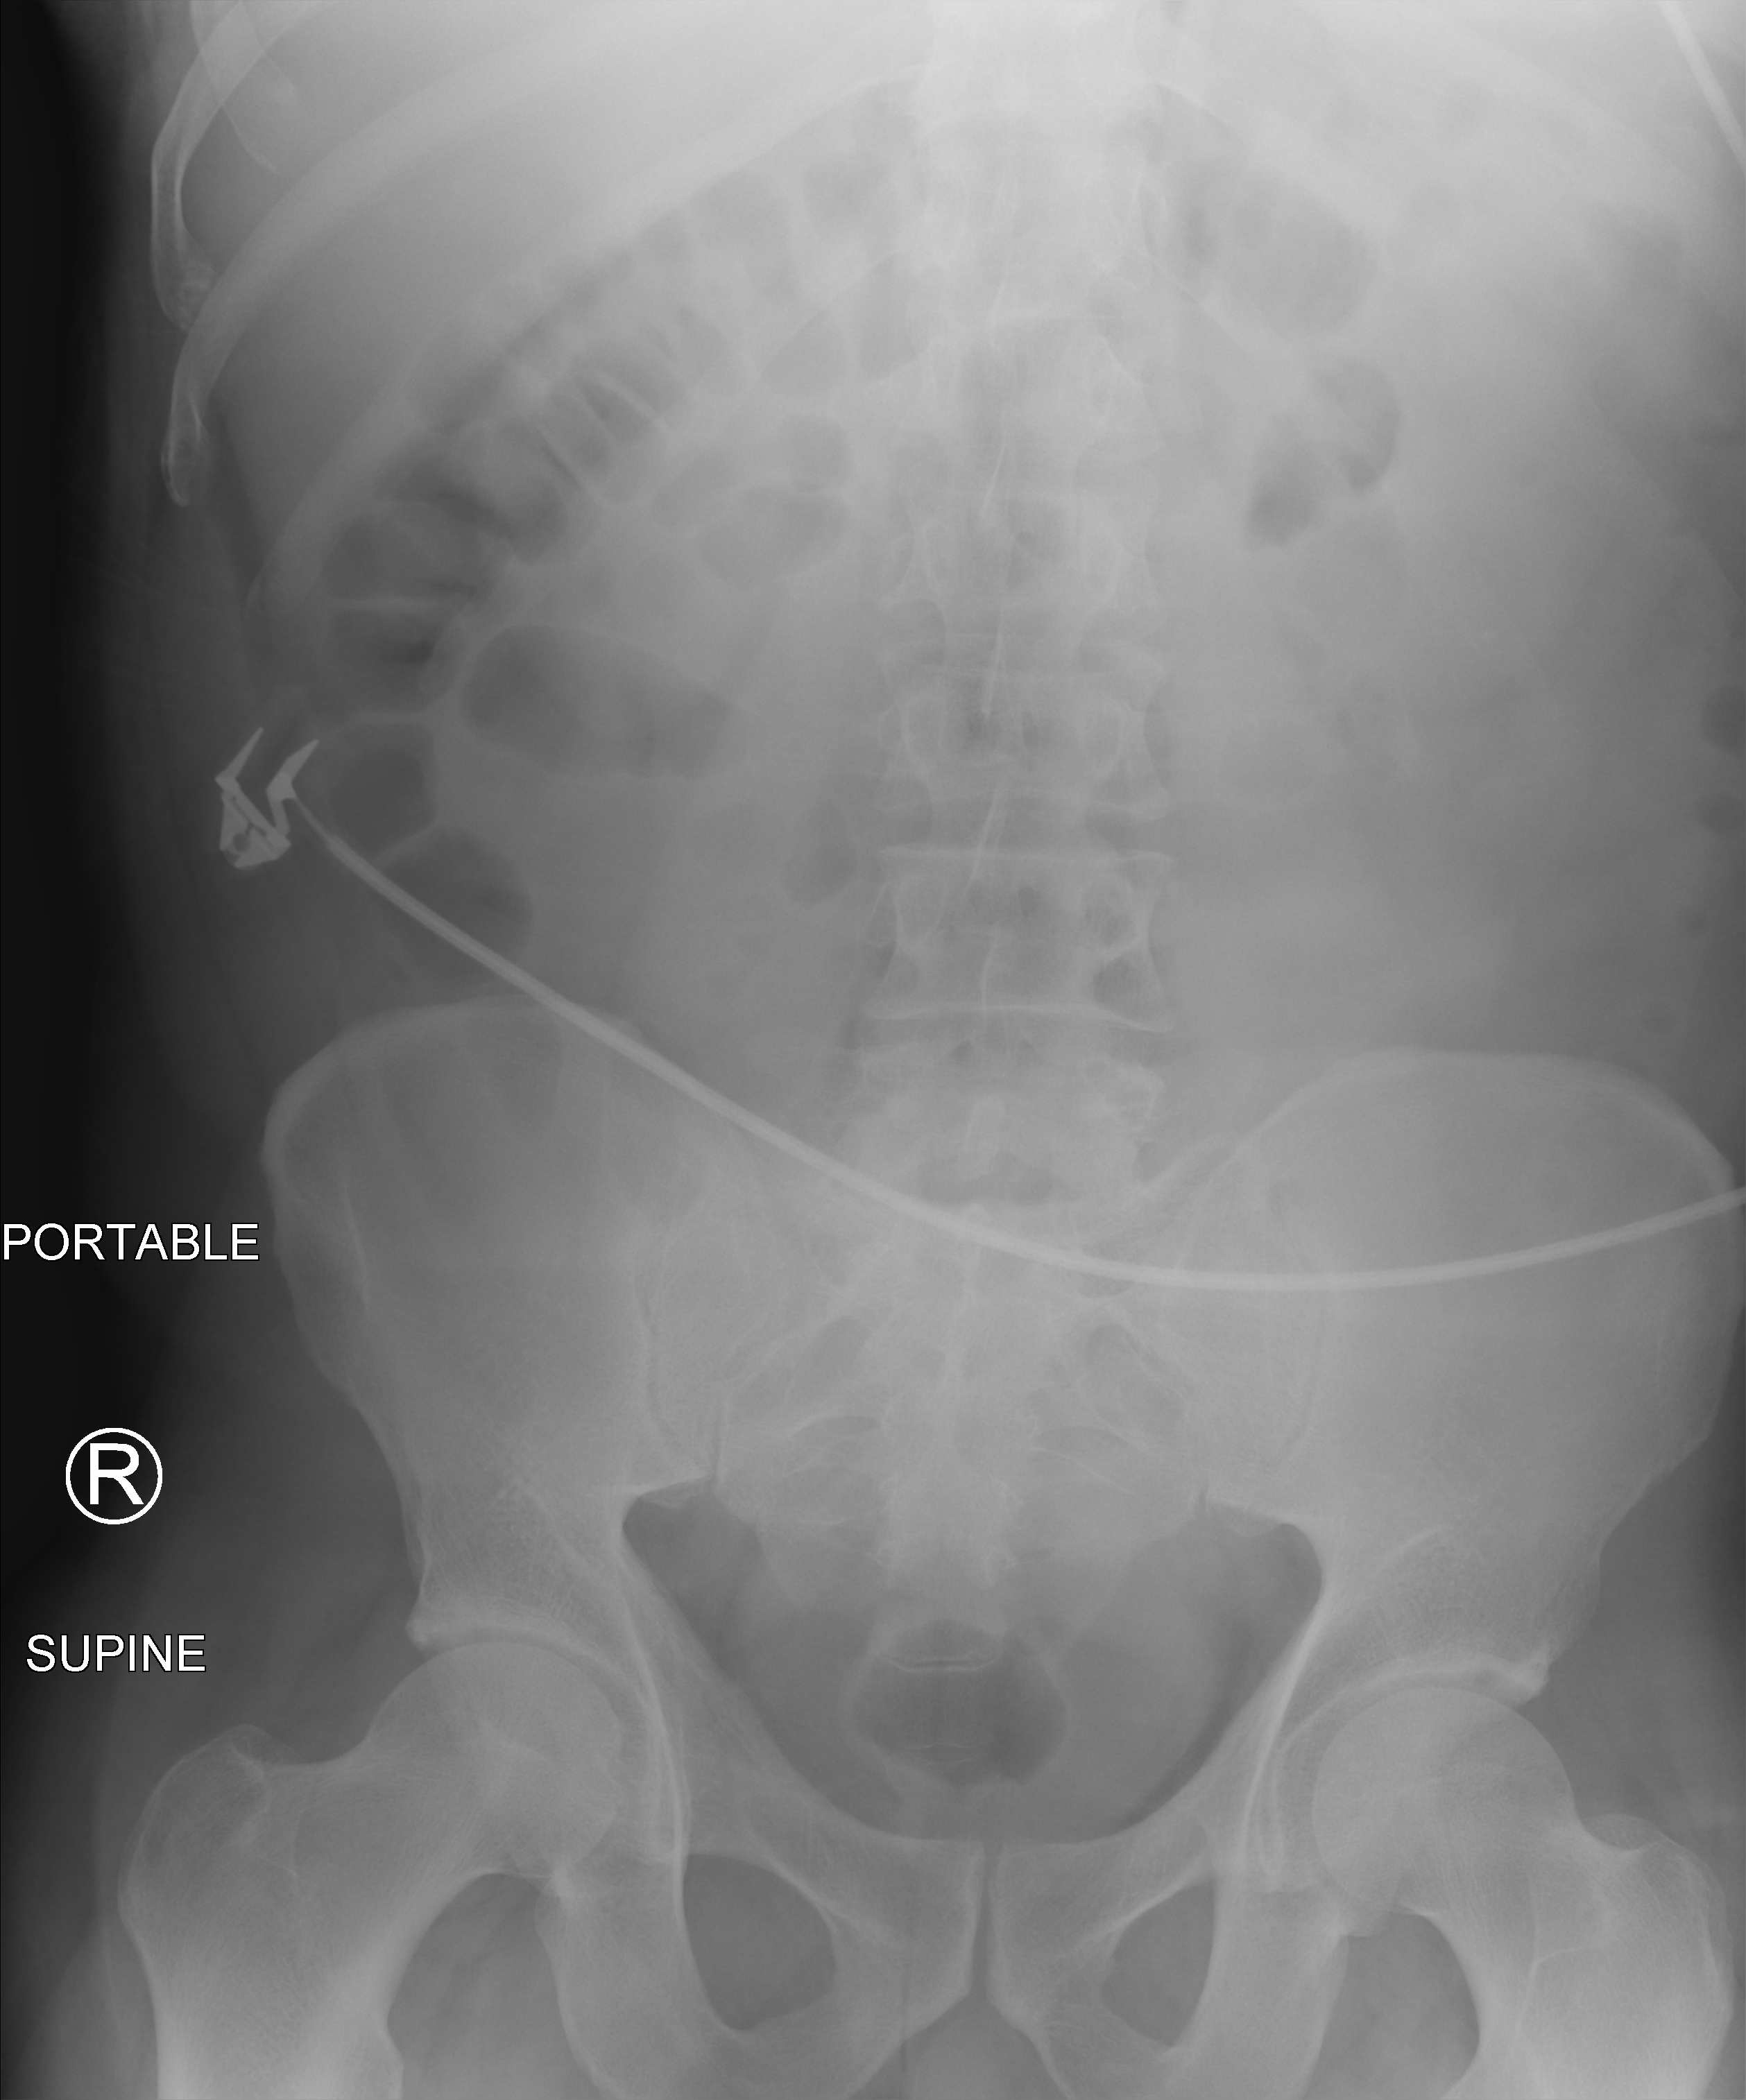
Abdomen X-ray (portable); anteroposterior (AP) projection. Male patient hospitalised with COVID-19, age 18–59 years.
From the hospital-stay record, not from the radiograph (when in the stay this image was taken is not recorded):
- COPD (admission record): no
- mechanically ventilated during this hospital stay: no